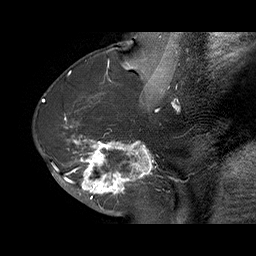
Breast MRI (dynamic contrast-enhanced), one sagittal slice; position 32 of 70 along the scan axis; dynamic contrast-enhanced series, time point 2 of 6 at this slice position (early post-contrast); 1.5 T; TE 4.5 ms, TR 32.4 ms; 3 mm slice thickness; 256 × 256 image matrix, field of view 180 × 180 mm. Female patient. From the clinical record (not read from this slice): setting: breast cancer imaged before/during neoadjuvant chemotherapy; receptor status: HR-positive, HER2-negative.
Outlined on this slice (semi-automatically segmented with operator editing):
- analysis volume of interest (the breast-tissue region the enhancement analysis was run in; not a lesion): bounding box [x1, y1, x2, y2] px = [71, 128, 159, 202]
- tumour enhancement mask (voxels above the 100 % enhancement threshold inside the analysis volume of interest): [71, 134, 153, 202]